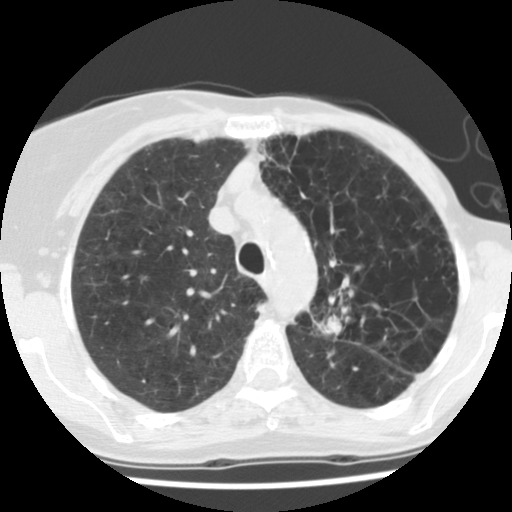
Axial slice from a low-dose chest CT screening exam. Baseline screening round. Lung window (W 1500 / L -600 HU). 140 kVp. Slice 34 of 128 in the series. Female participant, aged 67 years at enrolment. Current smoker at enrolment.
Lesion marked by an expert reader, box from (x=303, y=281) to (x=380, y=355) px. The screening reader recorded 2 non-calcified nodules or masses ≥4 mm on this exam (left upper lobe, left lower lobe); which of them this box marks is not recorded. Participant outcome: lung cancer diagnosed 109 days after this screen — adenocarcinoma, NOS, left upper lobe, poorly differentiated (G3), stage IIB (AJCC 6th edition), 45 mm at pathology.